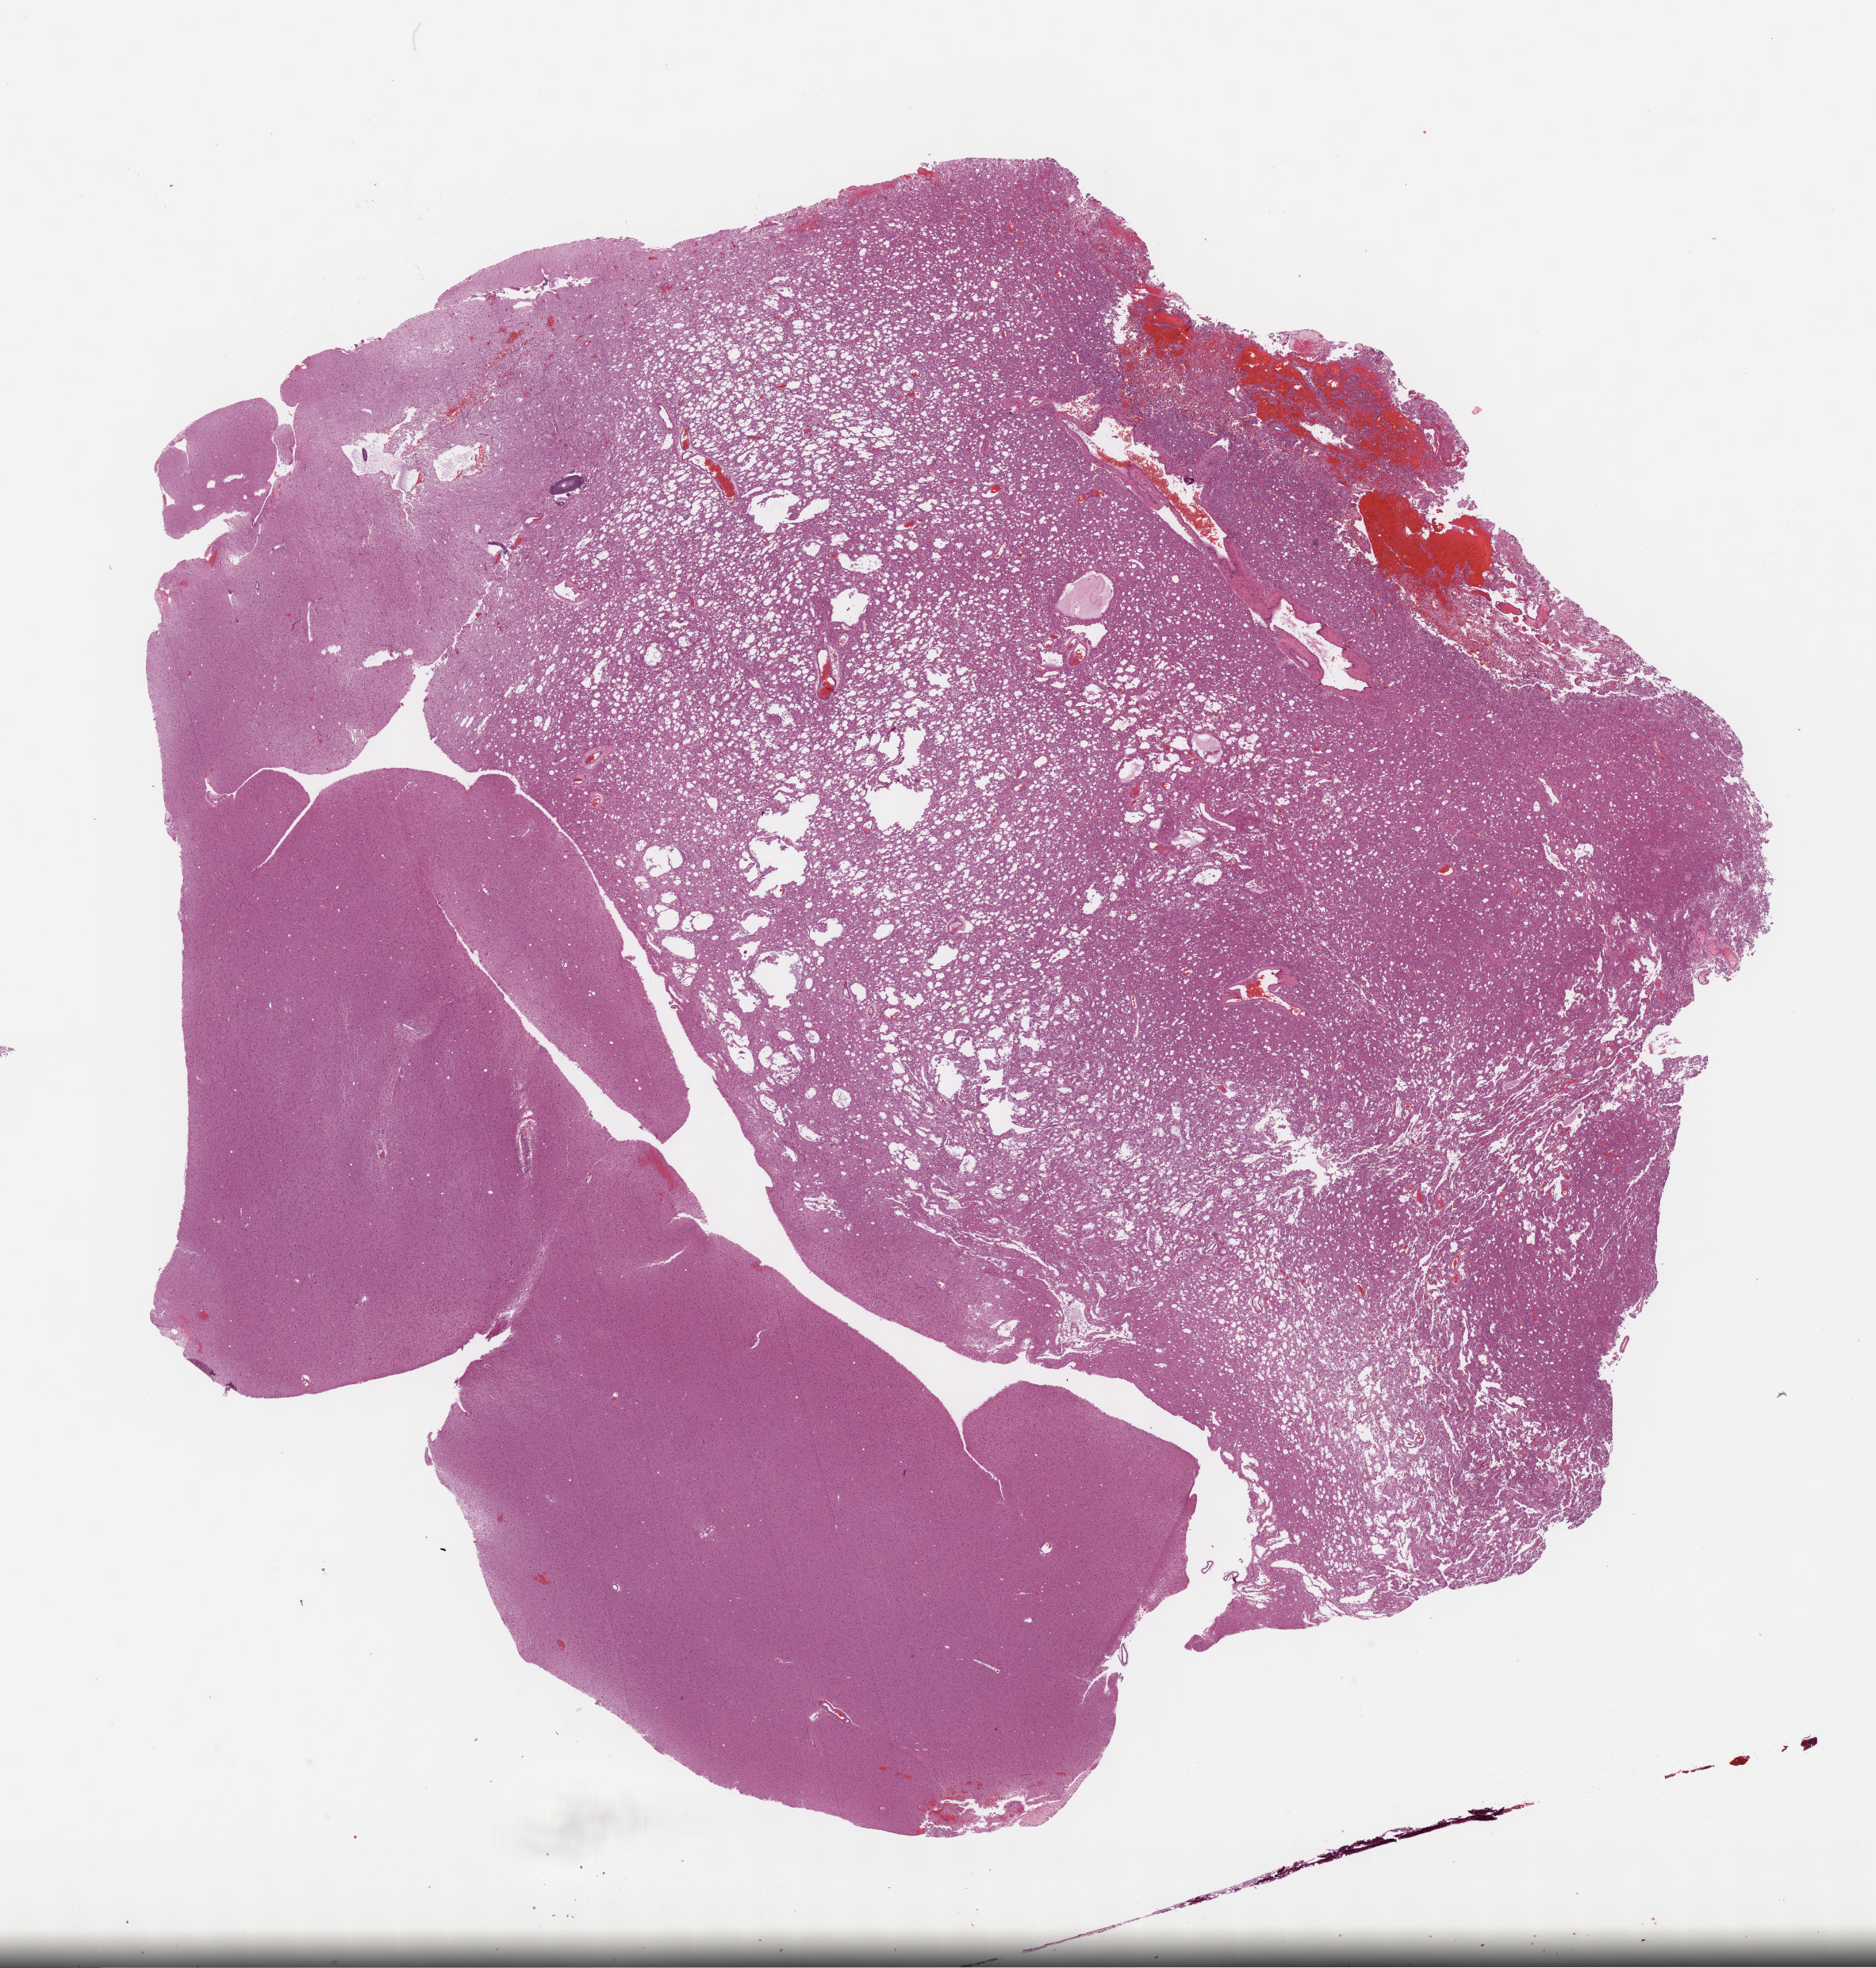
Digitized H&E tissue section (whole slide) — shown as a low-resolution overview of the whole scanned area (about 19.1 x 20.1 mm, from a 40x scan); formalin-fixed paraffin-embedded (FFPE) diagnostic section; brain, primary tumour sample. Male patient; age at initial diagnosis 61 years. Histologic grade: G2 (moderately differentiated).
Pathologic diagnosis: Mixed glioma (cerebrum). Laterality: right.